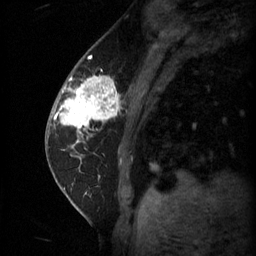
Breast MRI (dynamic contrast-enhanced), one sagittal slice. Position 18 of 60 along the scan axis. 3 images stored at this slice position (order not interpretable as contrast timing). 1.5 T. TE 4.2 ms, TR 11 ms. 256 × 256 image matrix, field of view 180 × 180 mm. Patient: female, 62 years.
Outlined on this slice (semi-automatically segmented with operator editing):
- analysis volume of interest (the breast-tissue region the enhancement analysis was run in; not a lesion): box from (x=55, y=72) to (x=123, y=133) px
- tumour enhancement mask (voxels above the 70 % enhancement threshold inside the analysis volume of interest): (x=56, y=76)–(x=121, y=133)